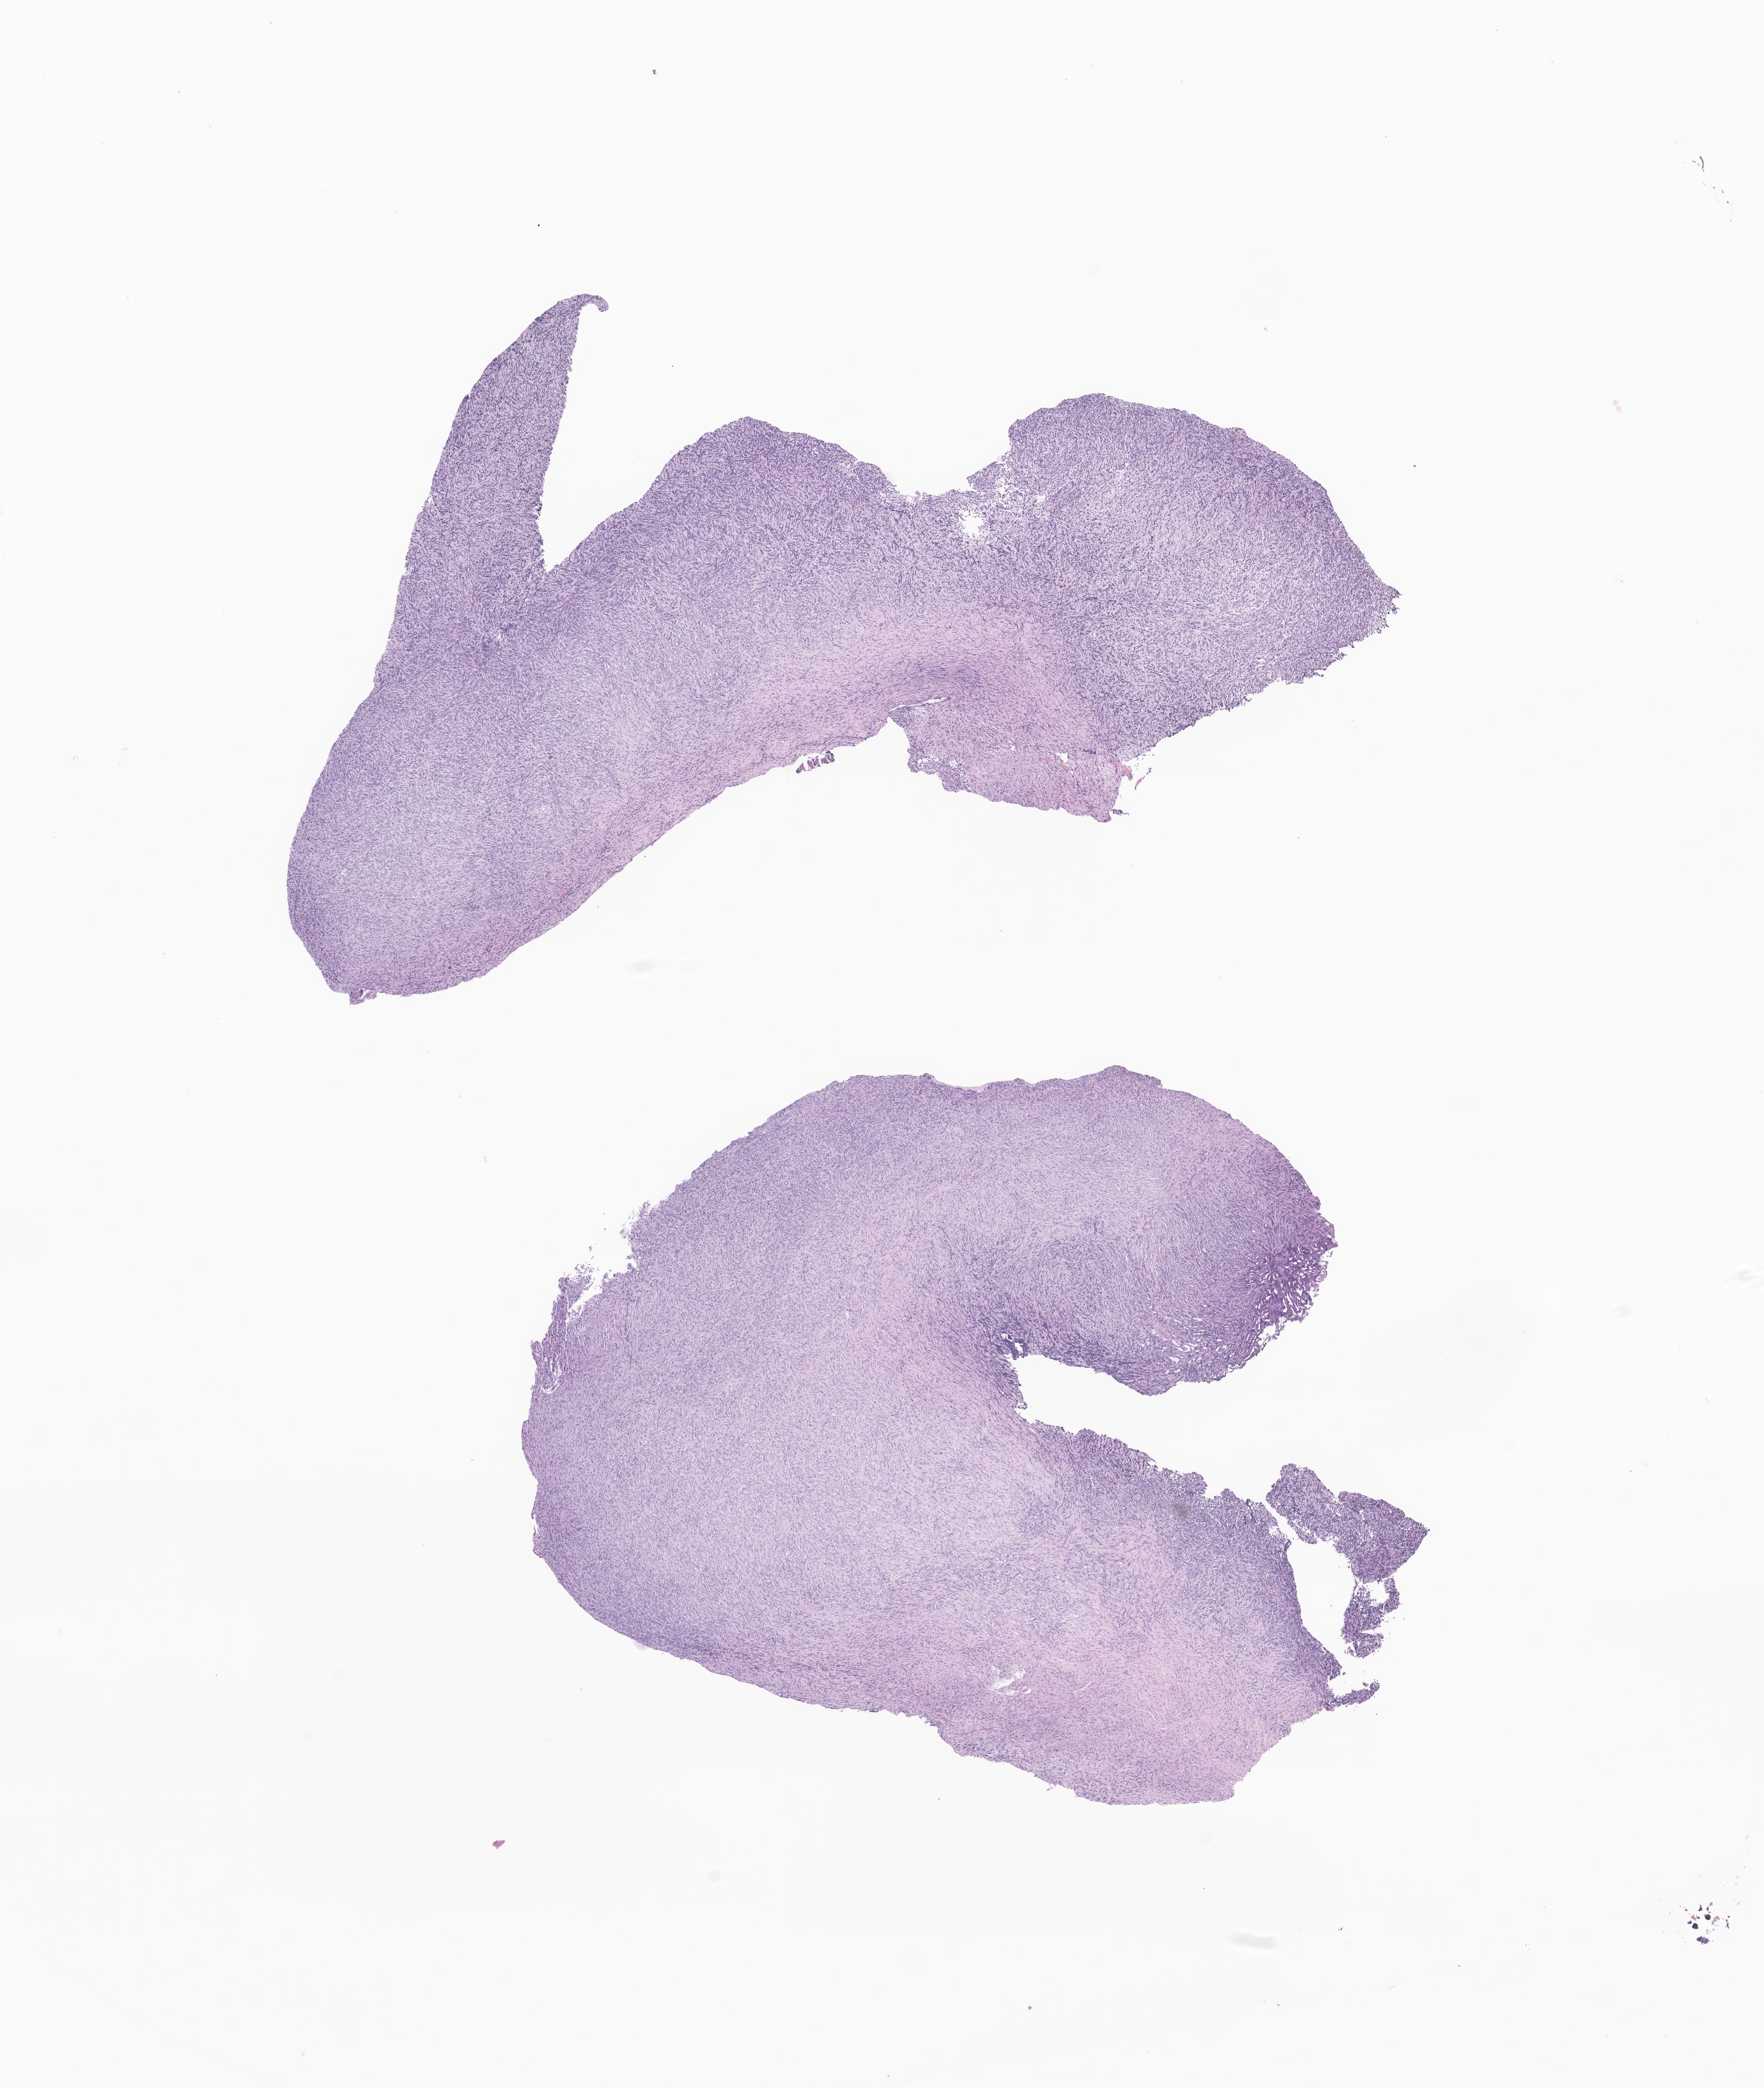
Haematoxylin and eosin whole-slide image of tumor tissue from the frontal lobe — shown as a low-resolution overview of the whole scanned area (about 11.4 x 13.5 mm), formalin-fixed paraffin-embedded section. Patient: female, age 143 days.
Diagnosis: Tumor cells, benign.